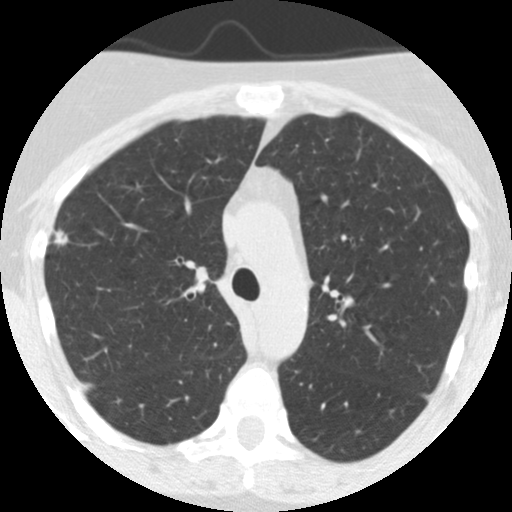
Axial slice from a low-dose chest CT screening exam, baseline annual screen, lung window (W 1500 / L -600 HU), standard (soft-tissue) reconstruction kernel (STANDARD), slice 171 of 249 in the series, 512 × 512 image matrix. Female participant, aged 55 years at enrolment. Current smoker at enrolment.
- Lesion marked by an expert reader, bounding box [x1, y1, x2, y2] px = [31, 219, 82, 267].
- The exam's reader record, not a measurement of the box and not confirmed to be the same lesion: non-calcified nodule or mass ≥4 mm, right upper lobe, 7 × 7 mm, spiculated (stellate) margins, soft tissue attenuation.
- Participant outcome: lung cancer diagnosed 1018 days after this screen (after the third annual screen) — bronchiolo-alveolar adenocarcinoma, NOS, right upper lobe, moderately differentiated (G2), stage IIA (AJCC 6th edition), 13 mm at pathology.